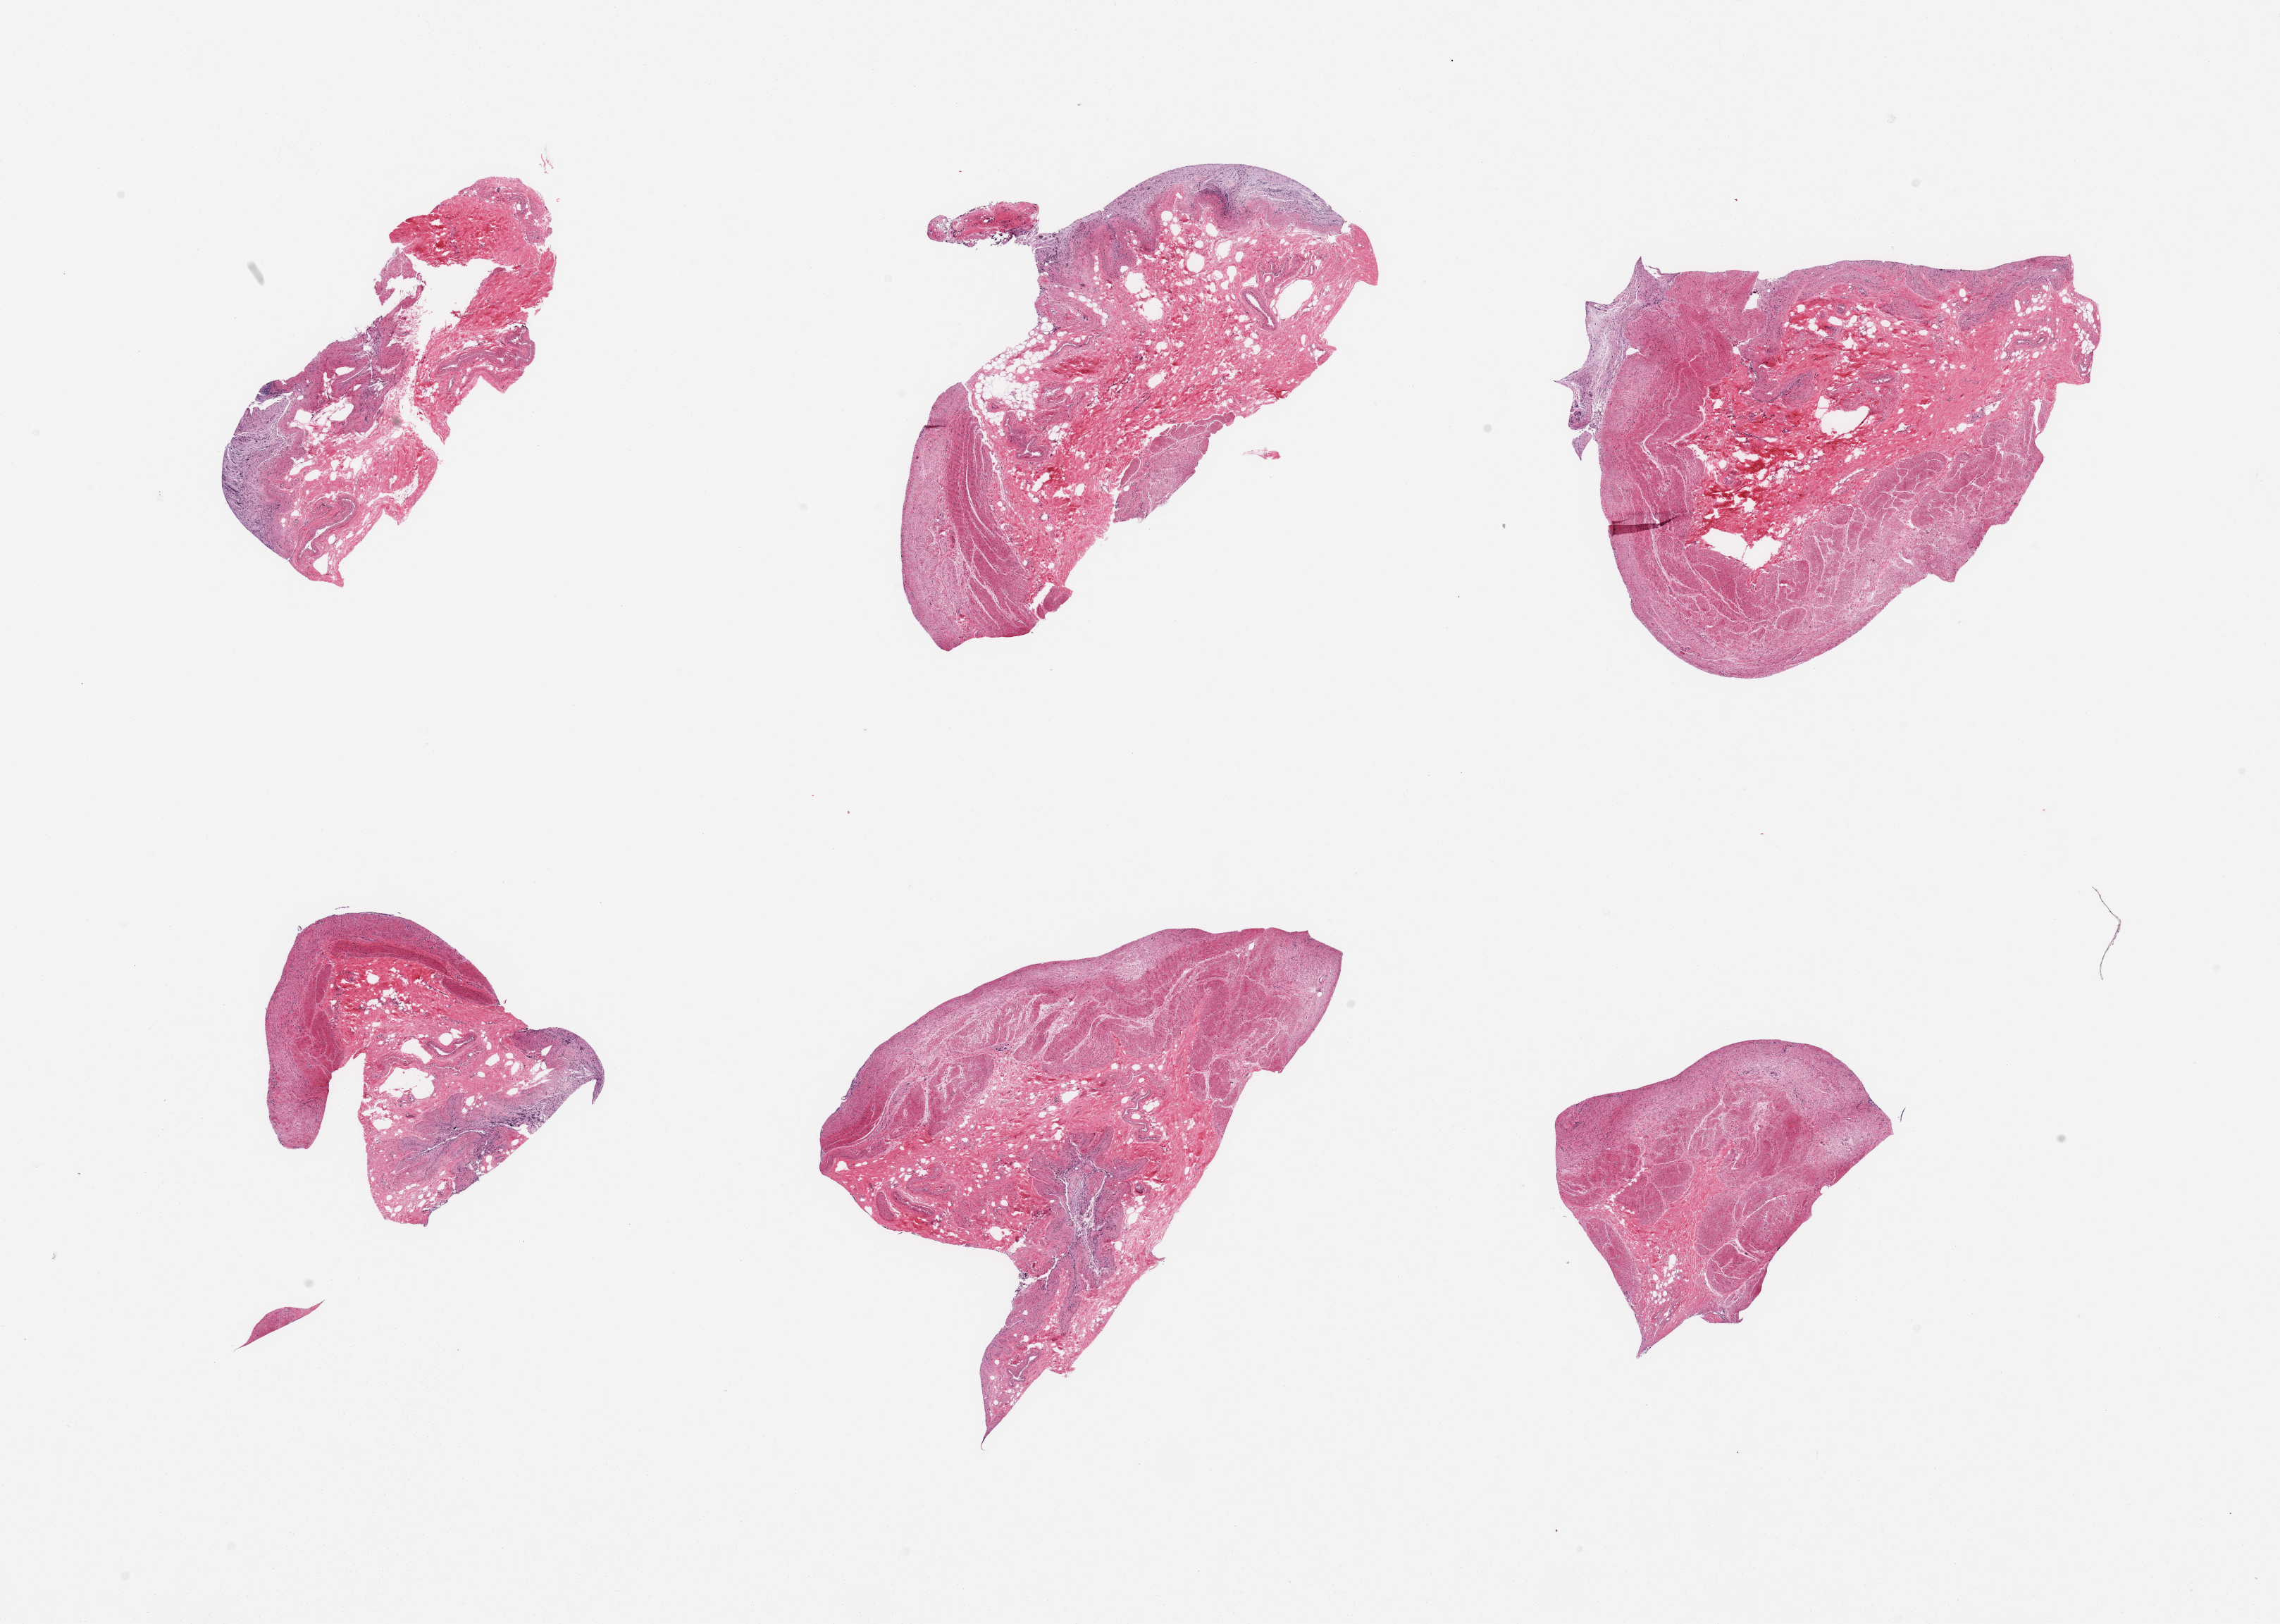
Digitized haematoxylin and eosin-stained section, brightfield — a low-resolution overview of the entire scanned area, about 25.6 x 18.2 mm (slide scanned at 20x), PAXgene-fixed paraffin-embedded (PFPE) section, sampled site (target tissue): stomach, tissue donor sample. Donor sex: male.
Pathologist's review note for this sample: 6 pieces, advanced autolysis.